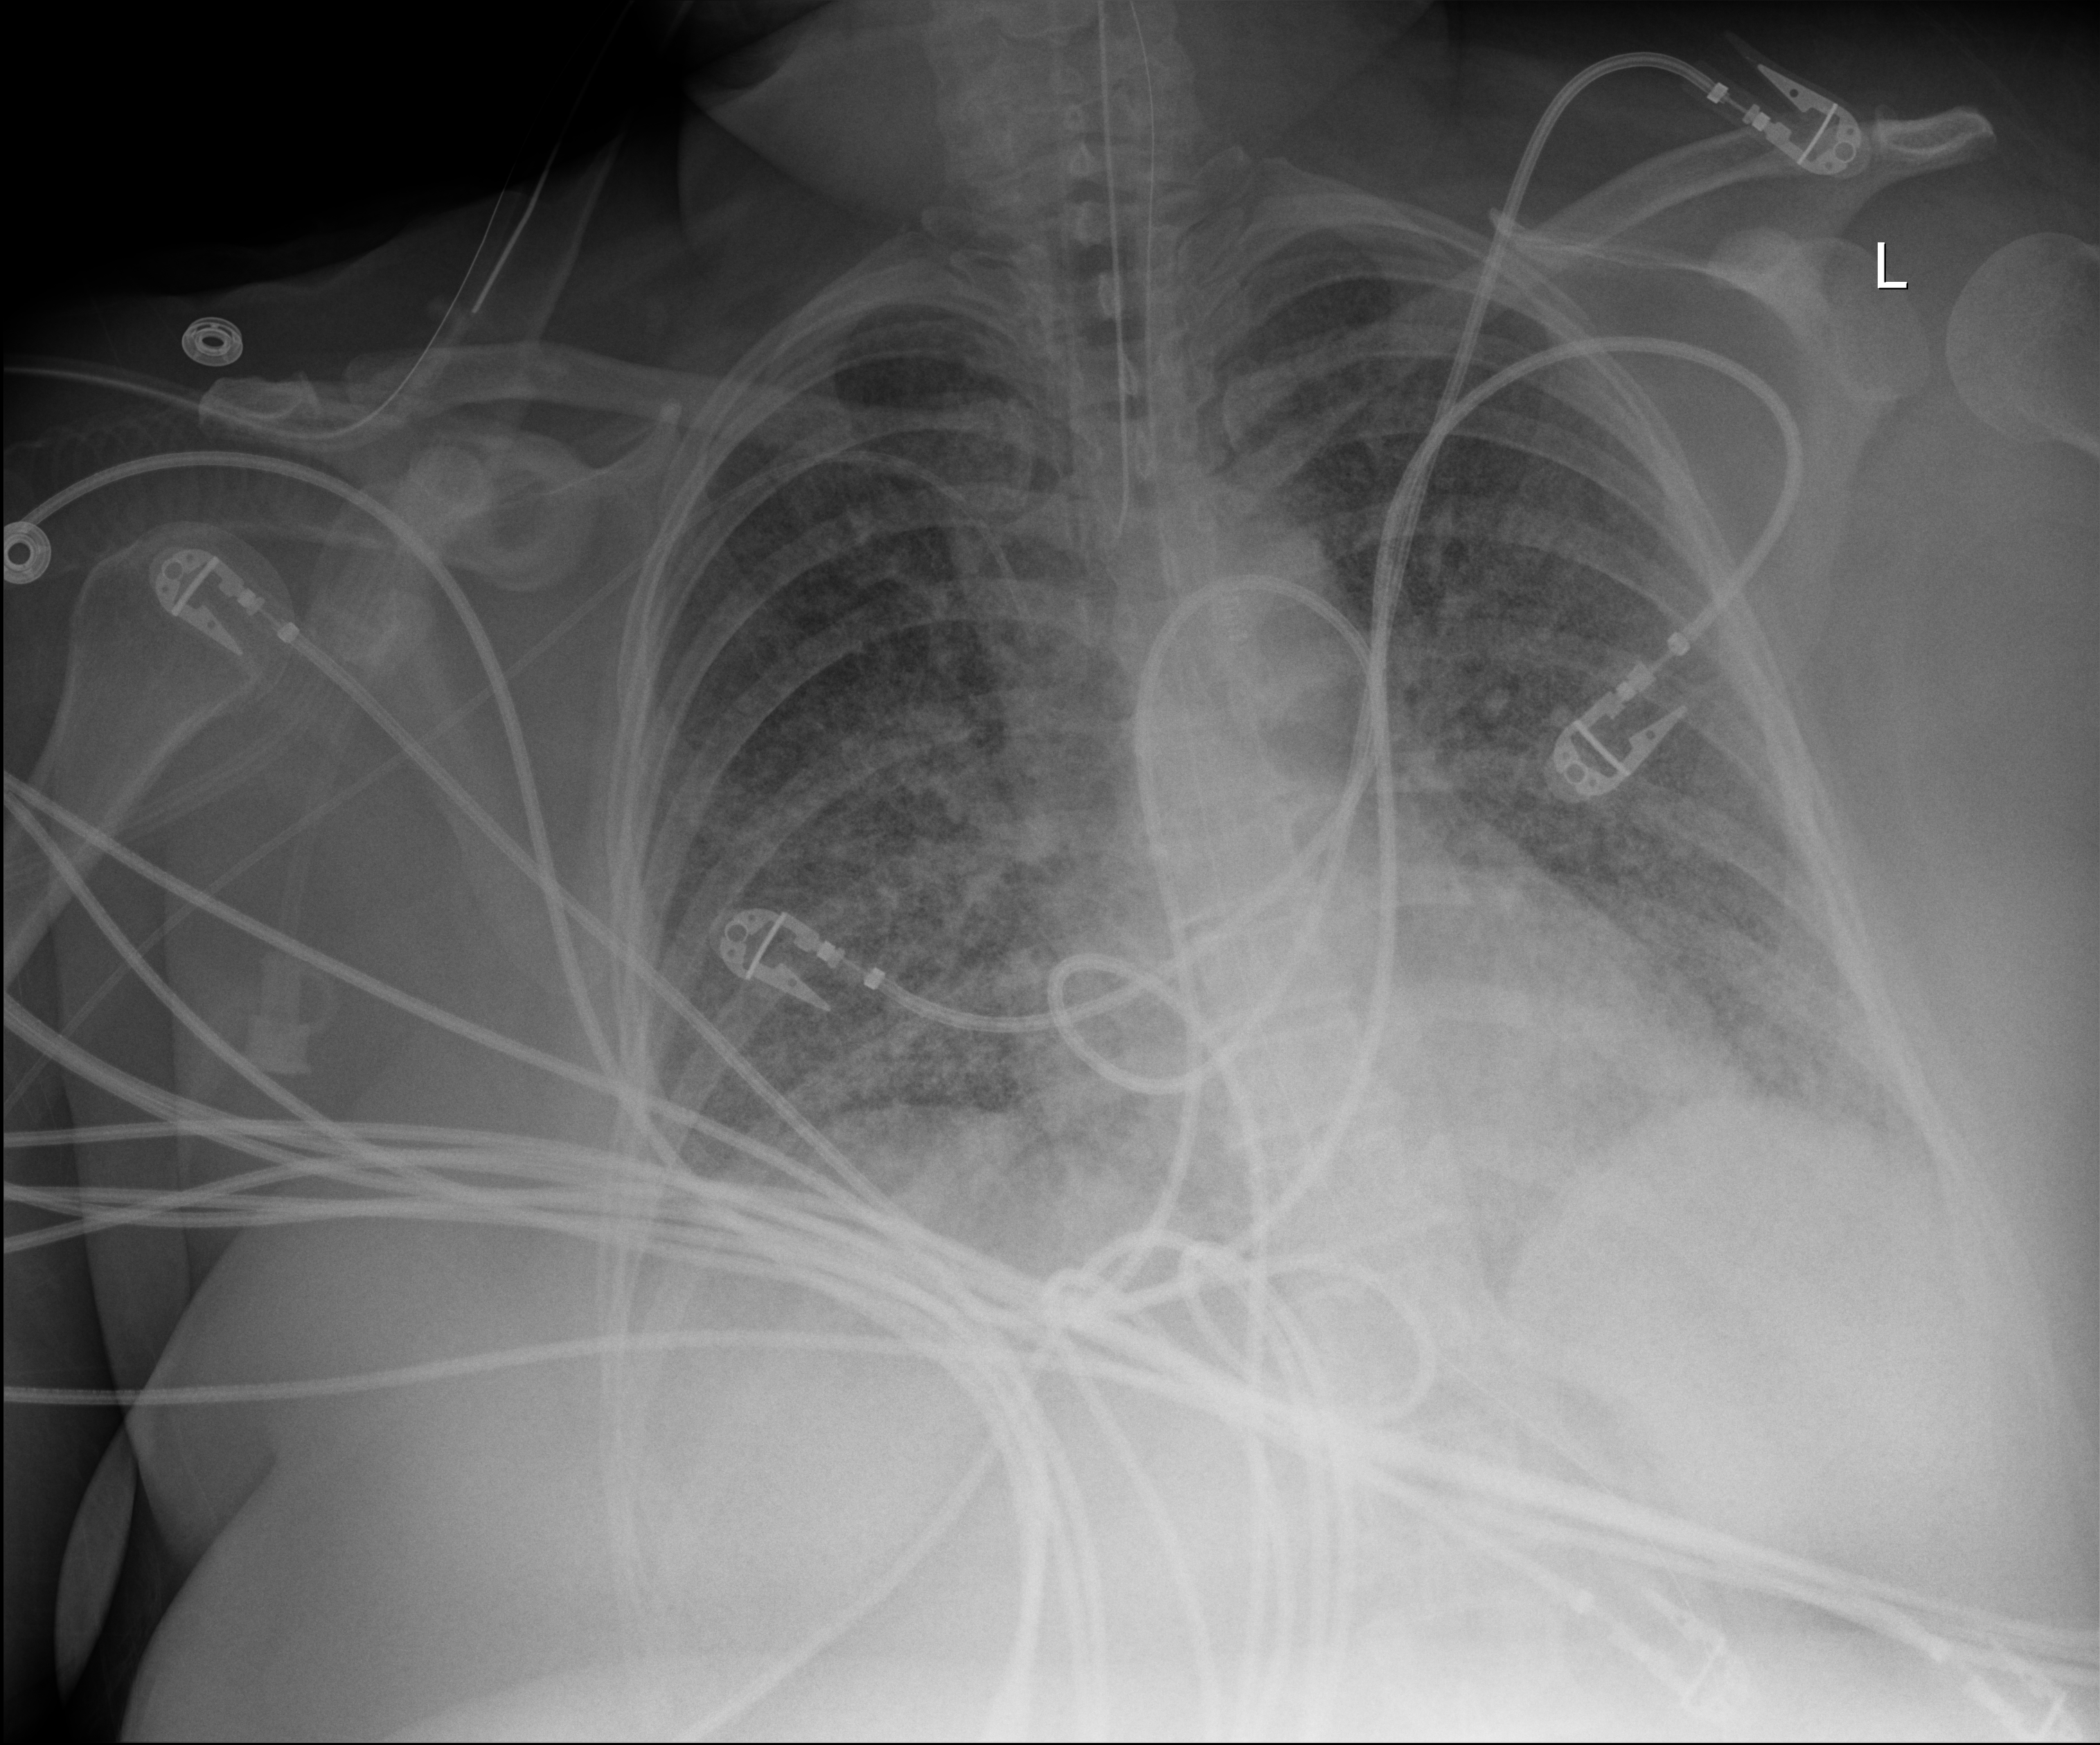
Bedside chest radiograph (digital radiography). Patient hospitalised with COVID-19; female, aged 18–59 years.
From the hospital-stay record, not from the radiograph (when in the stay this image was taken is not recorded): admitted to intensive care during this hospital stay: yes.